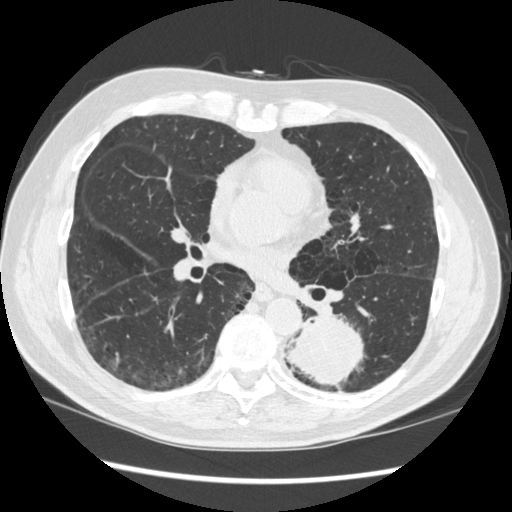
Low-dose screening chest CT, axial slice; baseline annual screen; lung window (W 1500 / L -600 HU); standard (soft-tissue) reconstruction kernel (STANDARD); 512 × 512 image matrix. Male participant, aged 72 years at enrolment. Current smoker at enrolment.
• Lesion marked by an expert reader, box from (x=266, y=304) to (x=370, y=396) px.
• The screening reader recorded 2 non-calcified nodules or masses ≥4 mm on this exam (left lower lobe, right middle lobe); which of them this box marks is not recorded.
• Participant outcome: lung cancer diagnosed 37 days after this screen — squamous cell carcinoma, NOS, left lower lobe, stage IIIA (AJCC 6th edition), 60 mm at pathology.